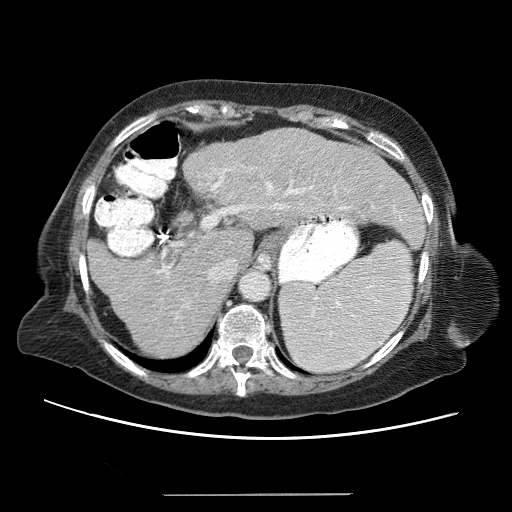
Contrast-enhanced abdominal CT (liver protocol), one axial slice; slice 42 of 65 in the series (ordered by position); soft-tissue window (W 400 / L 40 HU); 2.5 mm slice thickness; 512 × 512 image matrix, field of view 380 × 380 mm. From the clinical record (not read from this slice): diagnosis: hepatocellular carcinoma (patient treated with transarterial chemoembolisation; whether this scan precedes or follows treatment is not stated here); TNM stage (as recorded): Stage-IIIB; Child-Pugh class: A.
Outlined on this slice (semi-automatically segmented with operator editing):
- liver parenchyma outside the tumour (the mass and vessels are separate outlines, so this box may not span the whole liver): bounding box [x1, y1, x2, y2] px = [88, 128, 426, 354]
- liver vessels: [96, 152, 398, 336]